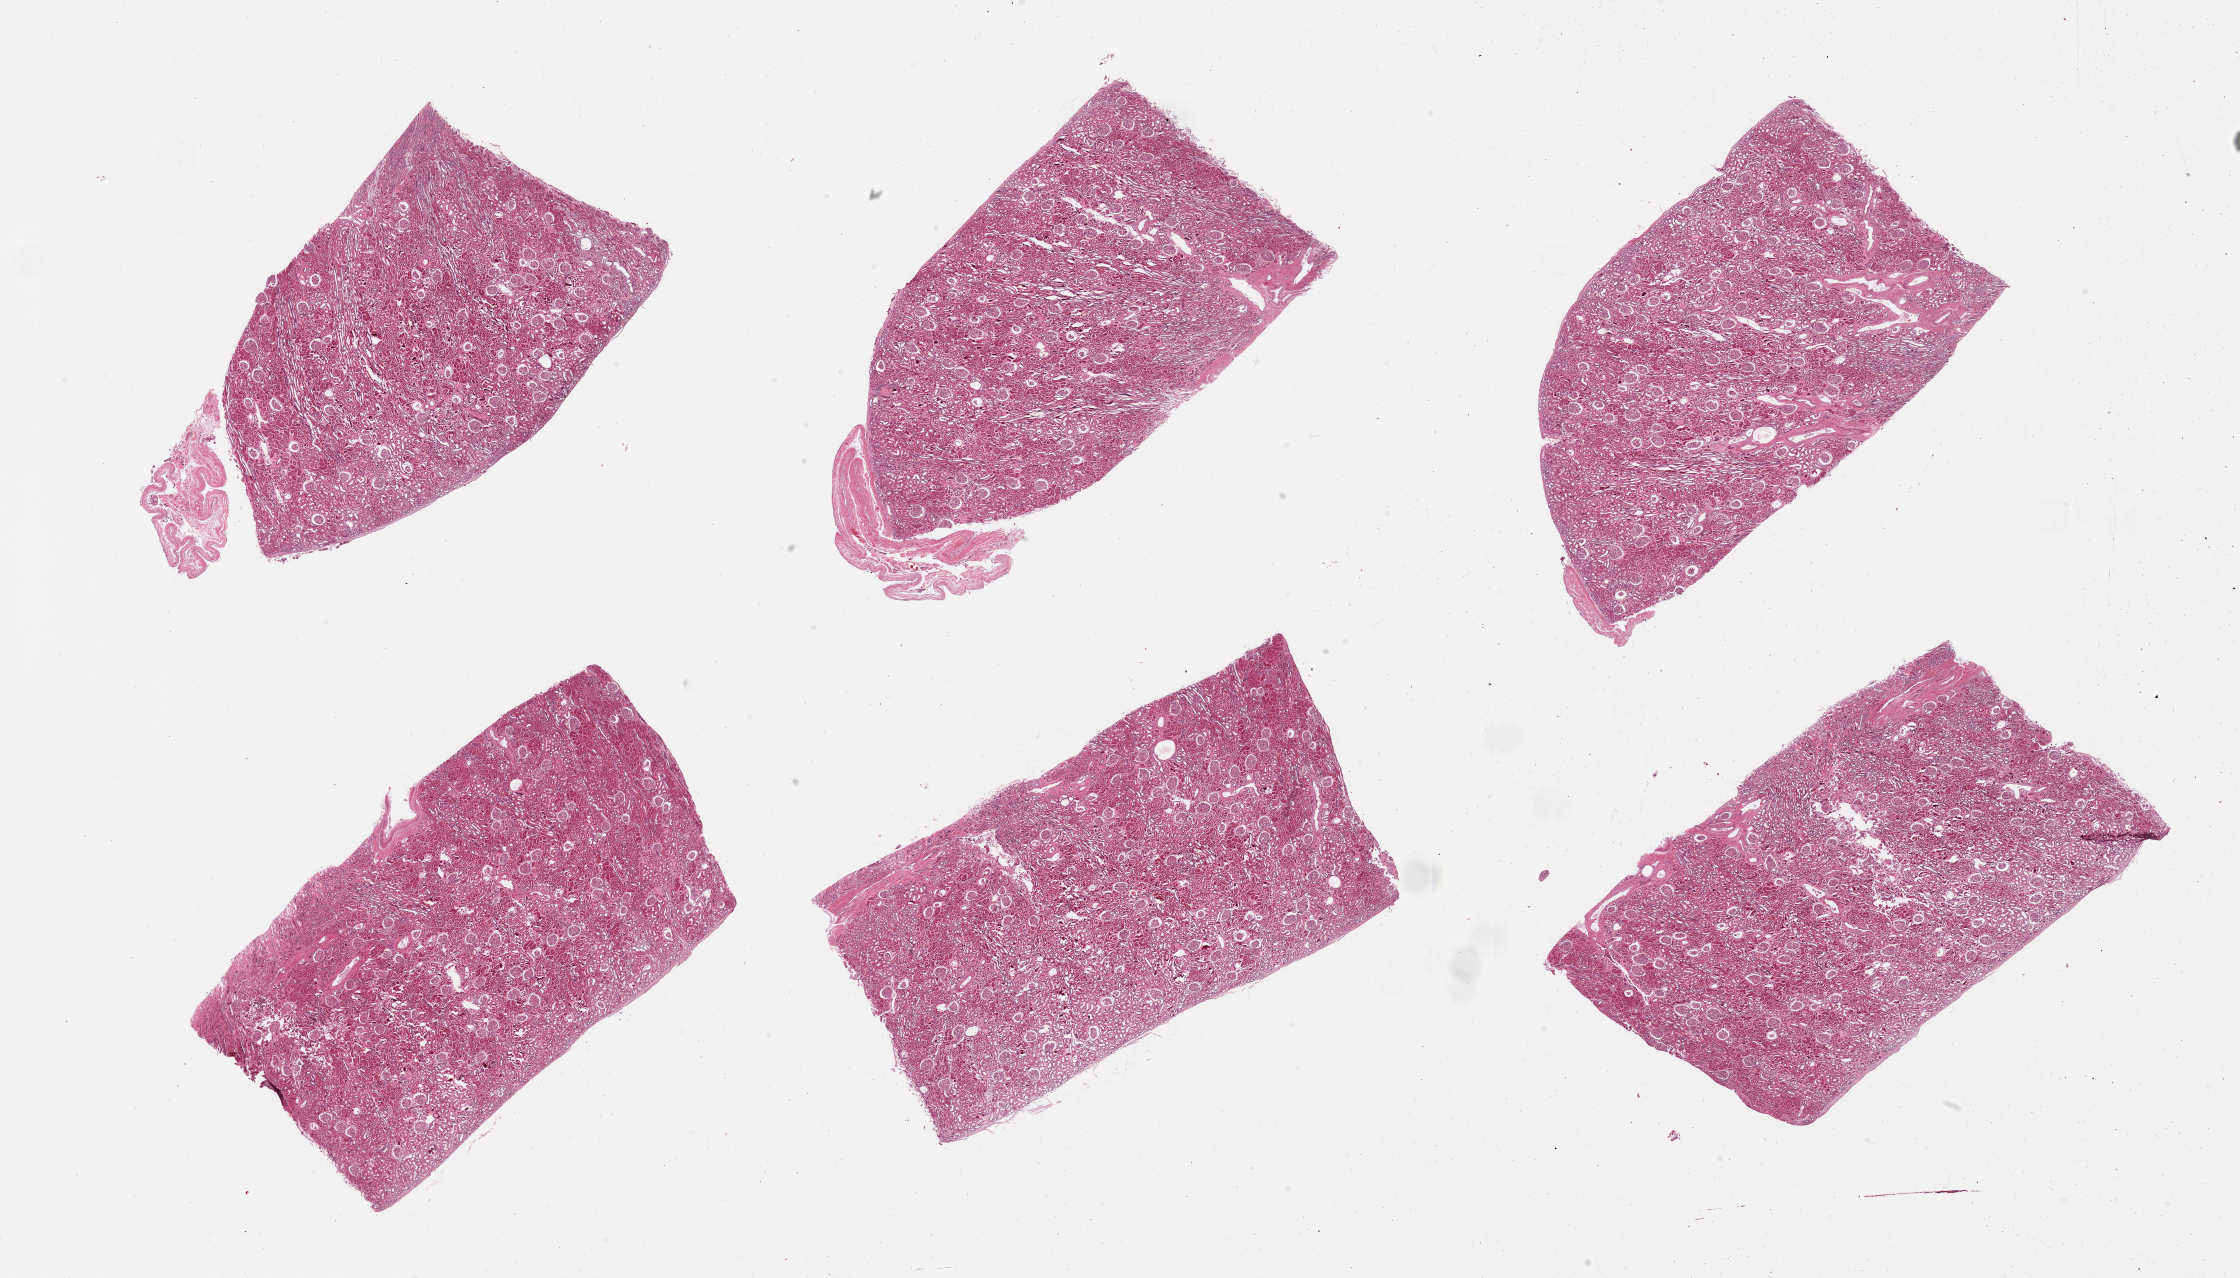
Digitized haematoxylin and eosin-stained section — whole scanned area (about 35.4 x 20.2 mm) shown as a low-resolution overview, PAXgene-fixed paraffin-embedded (PFPE) section, sampled site (target tissue): renal cortex, donor tissue sample. Donor sex: male.
* review note (as recorded): 6 pieces; no active or chronic lesions